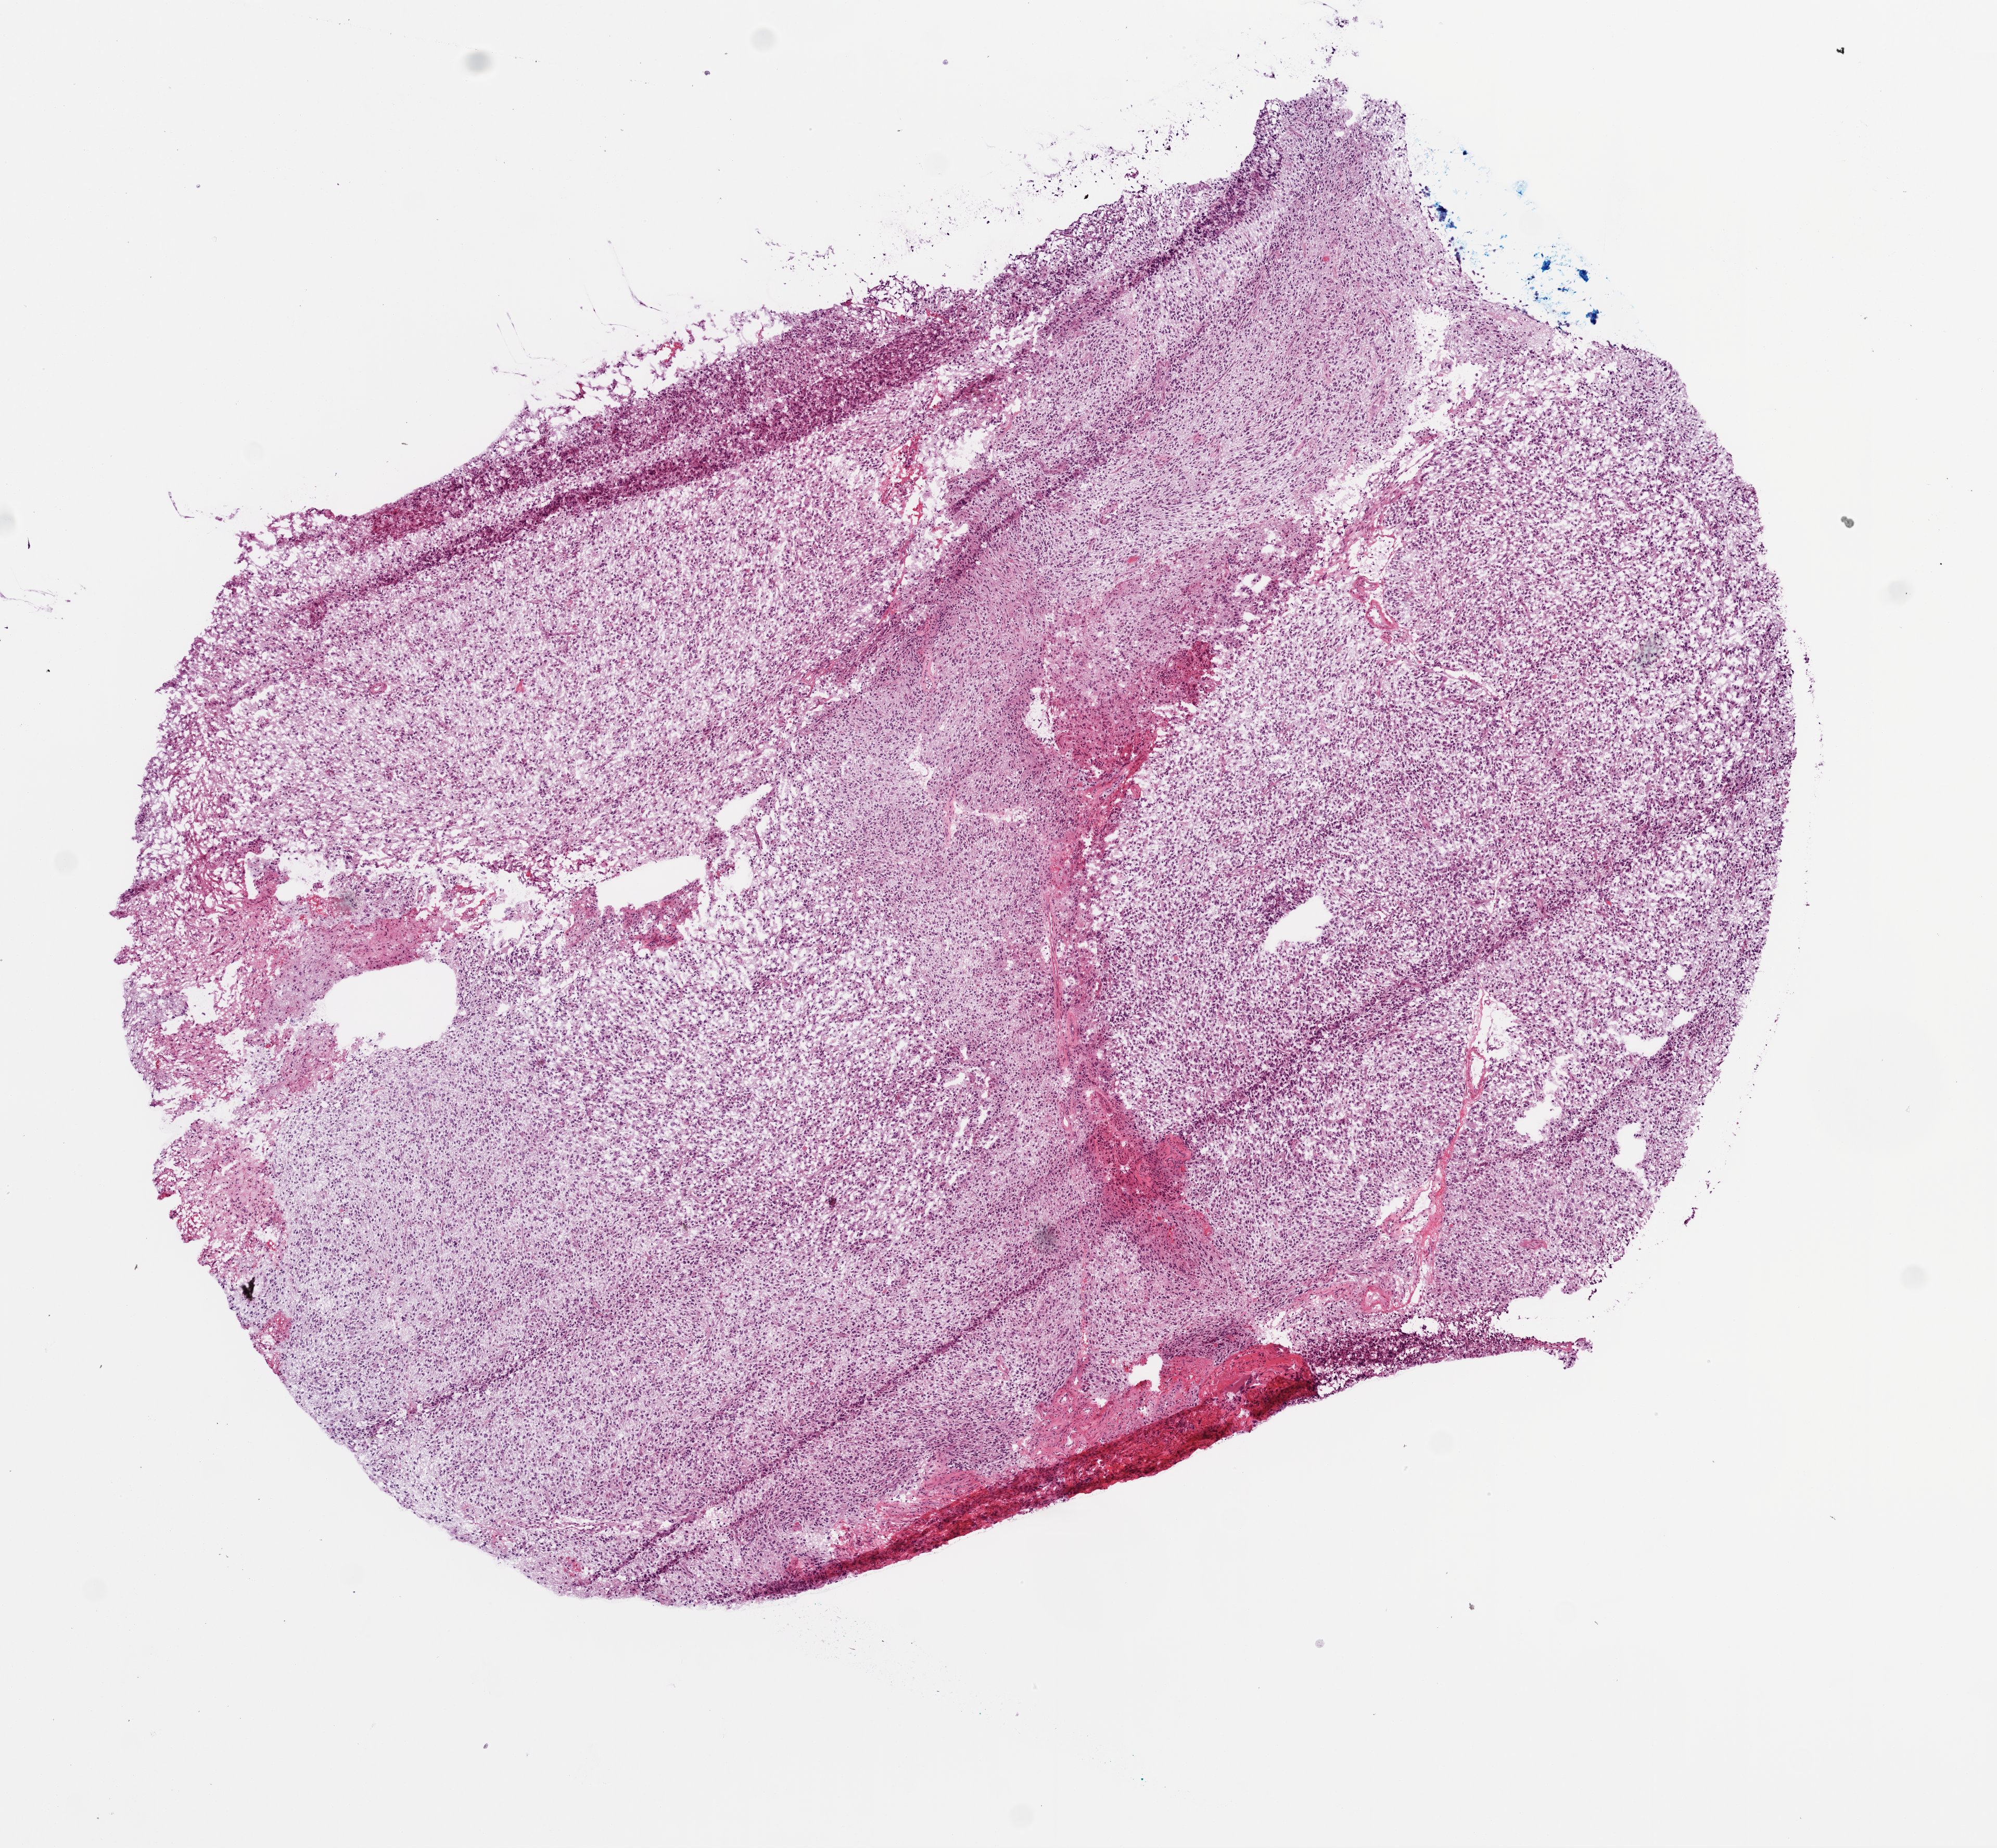
Whole-slide histology image, H&E, a low-resolution overview of the entire scanned area, about 7.7 x 7.2 mm (acquisition: 20x scan); frozen section; primary tumour sample from the brain. Male, age 66 years at initial diagnosis. Pathologist review of this section (percent, as recorded): tumour cells 95%, tumour nuclei 100%, normal cells 0%, stromal cells 0%, necrosis 5%.
Pathologic diagnosis: Glioblastoma.